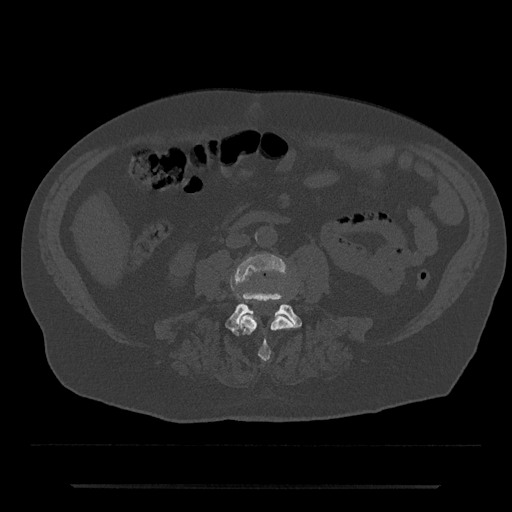
CT including the spine, one axial slice; position 378 of 797 along the scan axis; reconstruction kernel Br40s/3; bone window (W 1800 / L 400 HU); 0.5 mm slice thickness; 512 × 512 image matrix. Male patient, age 80 years. Case-level facts recorded for this patient, not image findings: primary cancer: prostate; vertebrae with lytic lesions (as recorded): L1, T11.
Outlined on this slice (semi-automatic segmentation, software-assisted and operator-edited):
- L3 vertebra: bounding box [x1, y1, x2, y2] px = [231, 254, 294, 361]
- L4 vertebra: [225, 292, 302, 335]